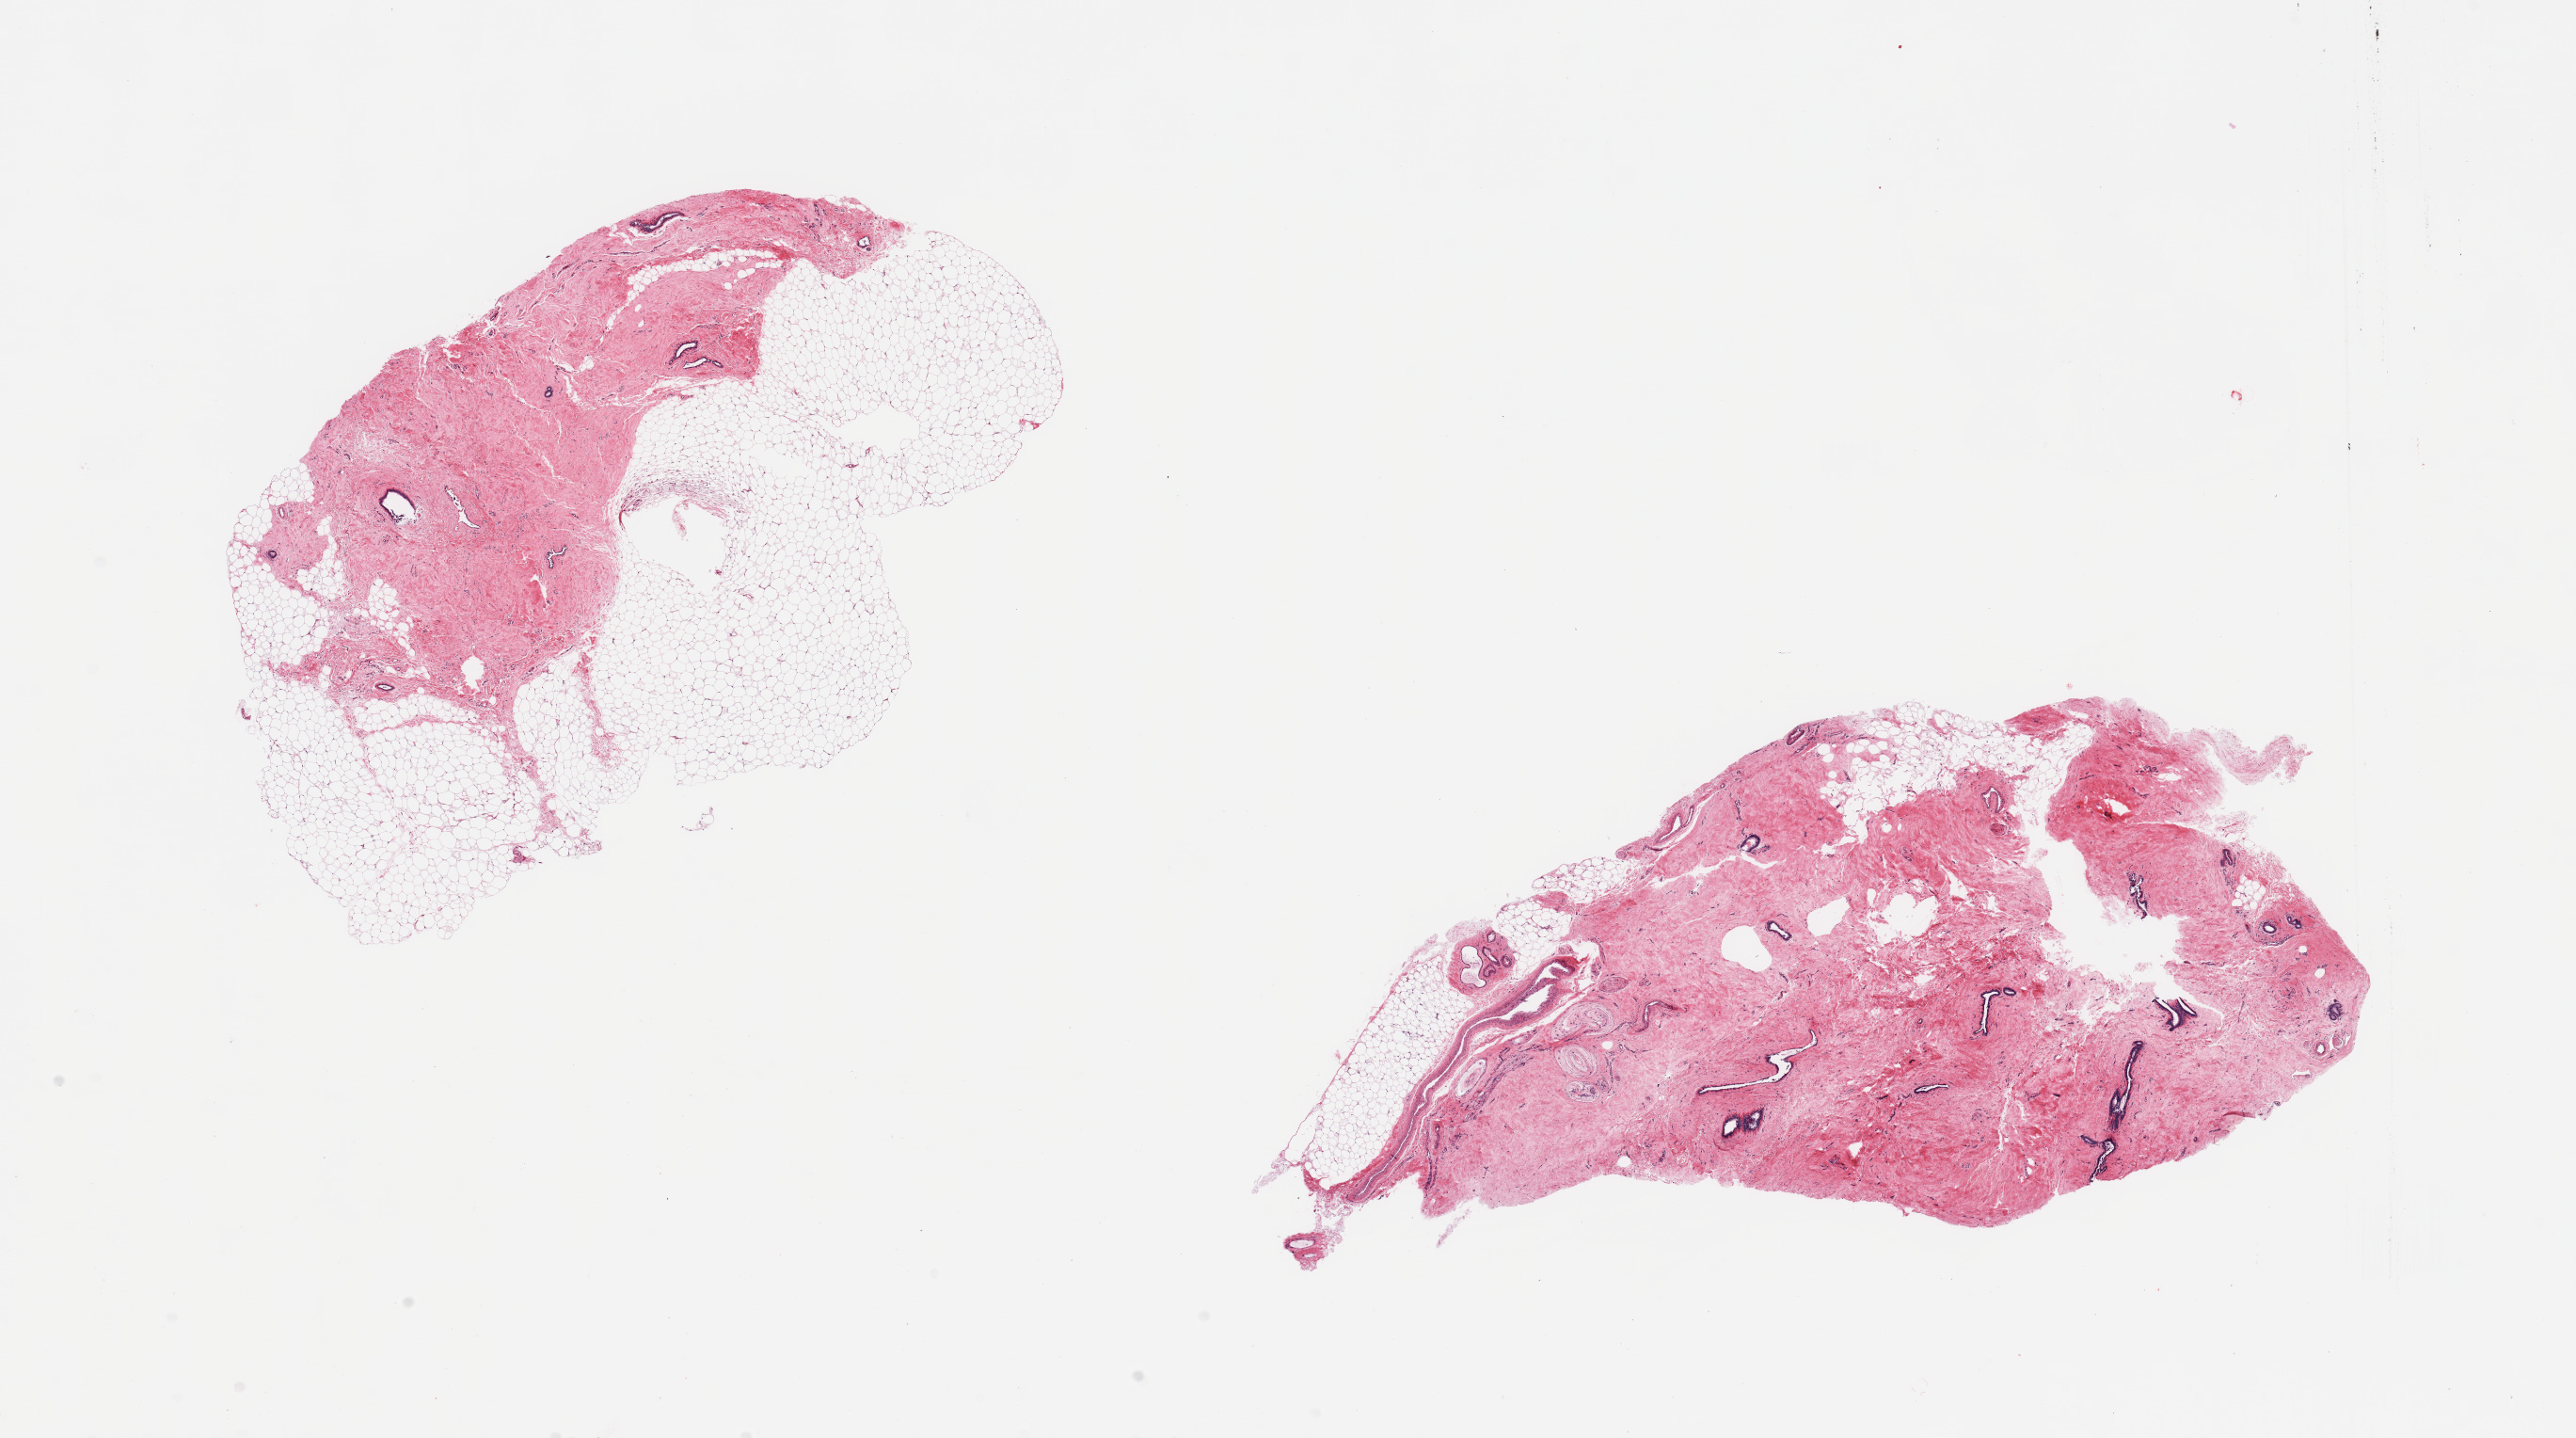
Haematoxylin and eosin whole-slide image, a low-resolution overview of the entire scanned area, about 21.7 x 12.1 mm (from a 20x scan). PAXgene-fixed paraffin-embedded (PFPE) section. Sampled site (target tissue): breast. Donor tissue sample. Male donor.
Reviewer comment on this tissue sample: 2 pieces, gynecomastoid stromal and ductal hyperplasia.